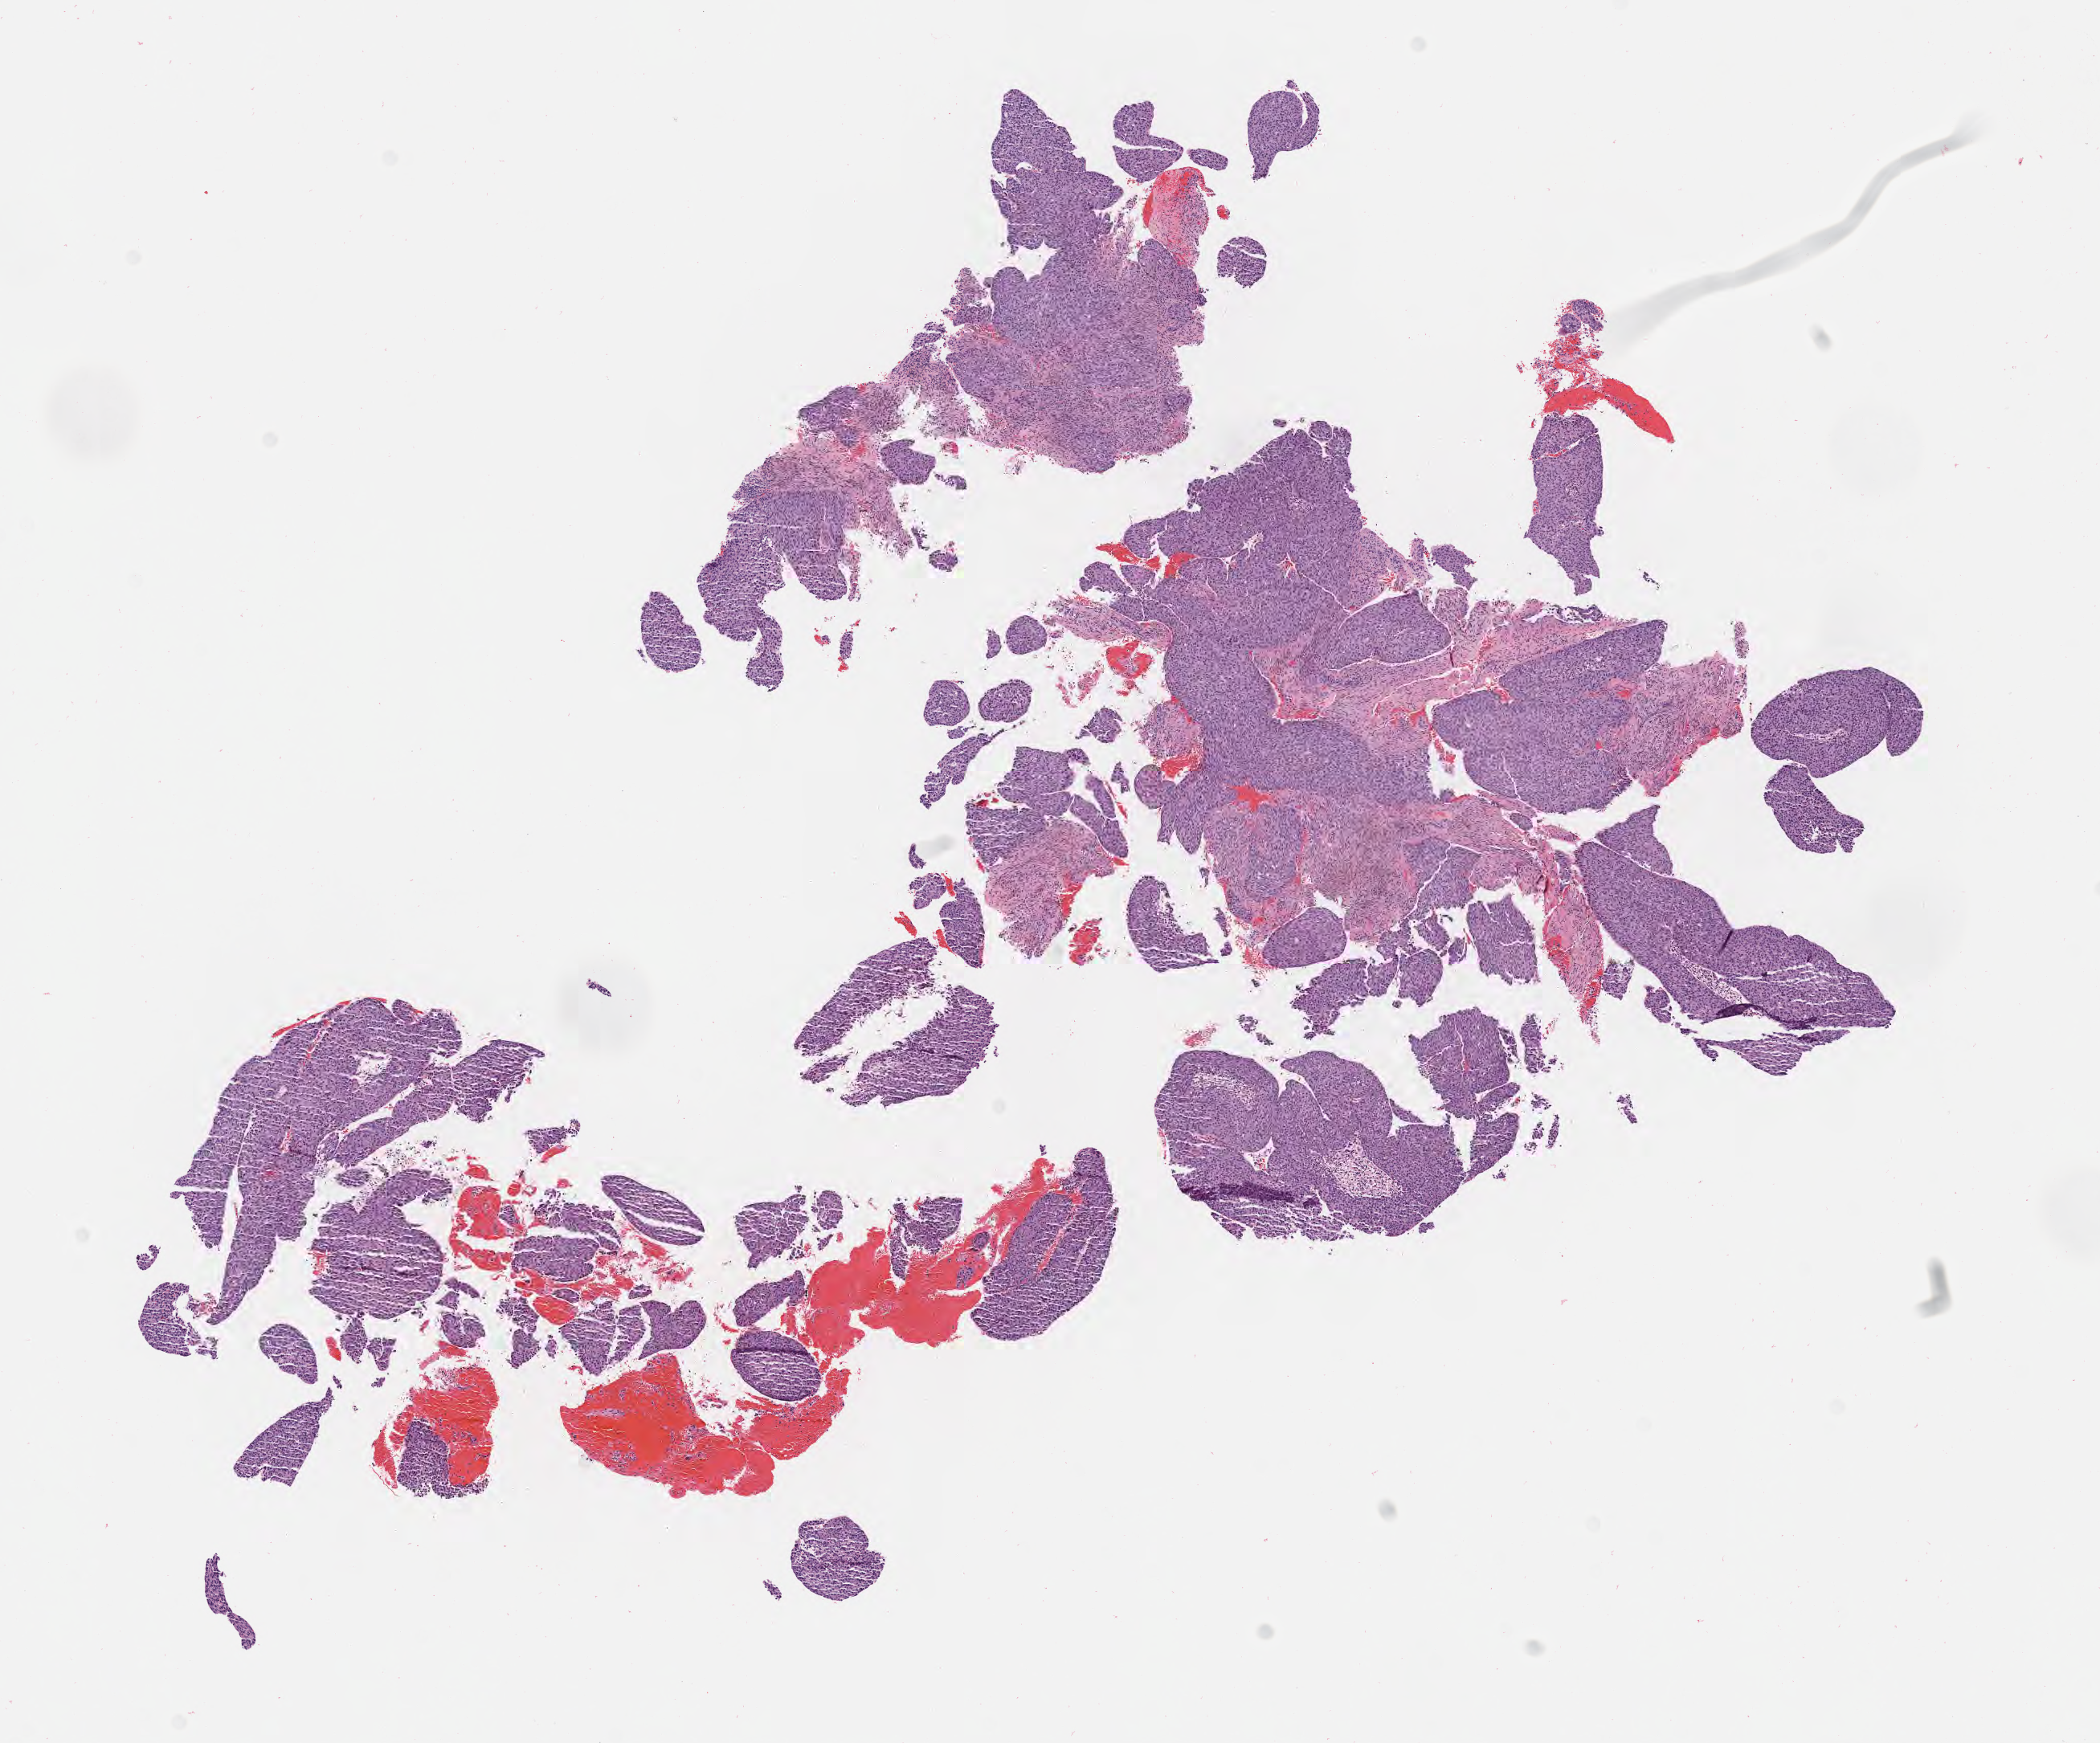
Digitized hematoxylin and eosin (H&E)-stained section — low-resolution overview of the scanned area, about 10.6 x 8.8 mm, specimen: tumor tissue, anatomic site: cervix. Patient: female, aged 53.
Histologic diagnosis: Squamous cell carcinoma, large cell, nonkeratinizing, NOS.